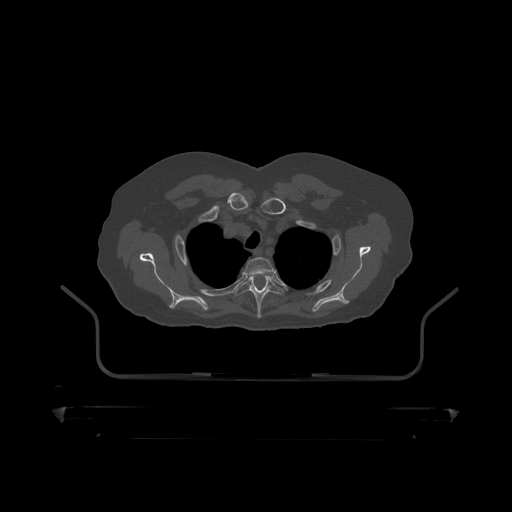
CT including the spine, one axial slice. 120 kVp. Bone window (W 1800 / L 400 HU). 1.25 mm slice thickness. 512 × 512 image matrix. Patient: male, 60 years. Case-level facts recorded for this patient, not image findings: primary cancer: prostate.
Structures marked on this image (semi-automatic segmentation, software-assisted and operator-edited):
- T2 vertebra: bounding box <244,258,275,276> (left, top, right, bottom; pixels)
- T3 vertebra: <235,275,284,319>